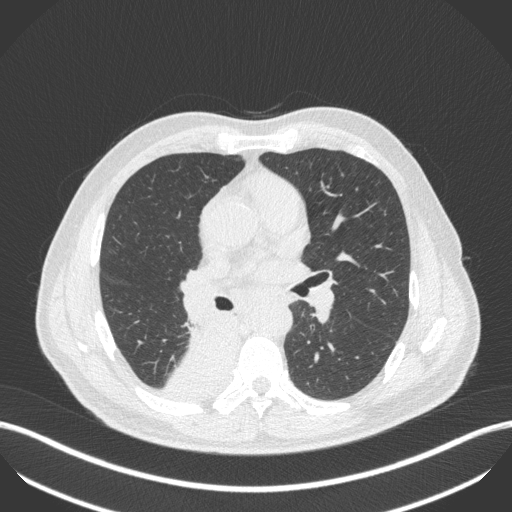
Chest CT, one axial slice. Position 260 of 451 along the scan axis. Lung window (W 1500 / L -600 HU). 1 mm slice thickness. 512 × 512 image matrix, field of view 400 × 400 mm. Patient: male, 61 years. Case-level facts recorded for this patient, not image findings: clinical TNM (as recorded): T1 N0 M0; histopathological grade: G3.
Structures marked on this image (rectangle marked by the reading radiologist):
- lung tumour (recorded histology: small cell carcinoma): bounding box (x1, y1, x2, y2) in pixels: (162, 323, 243, 397)